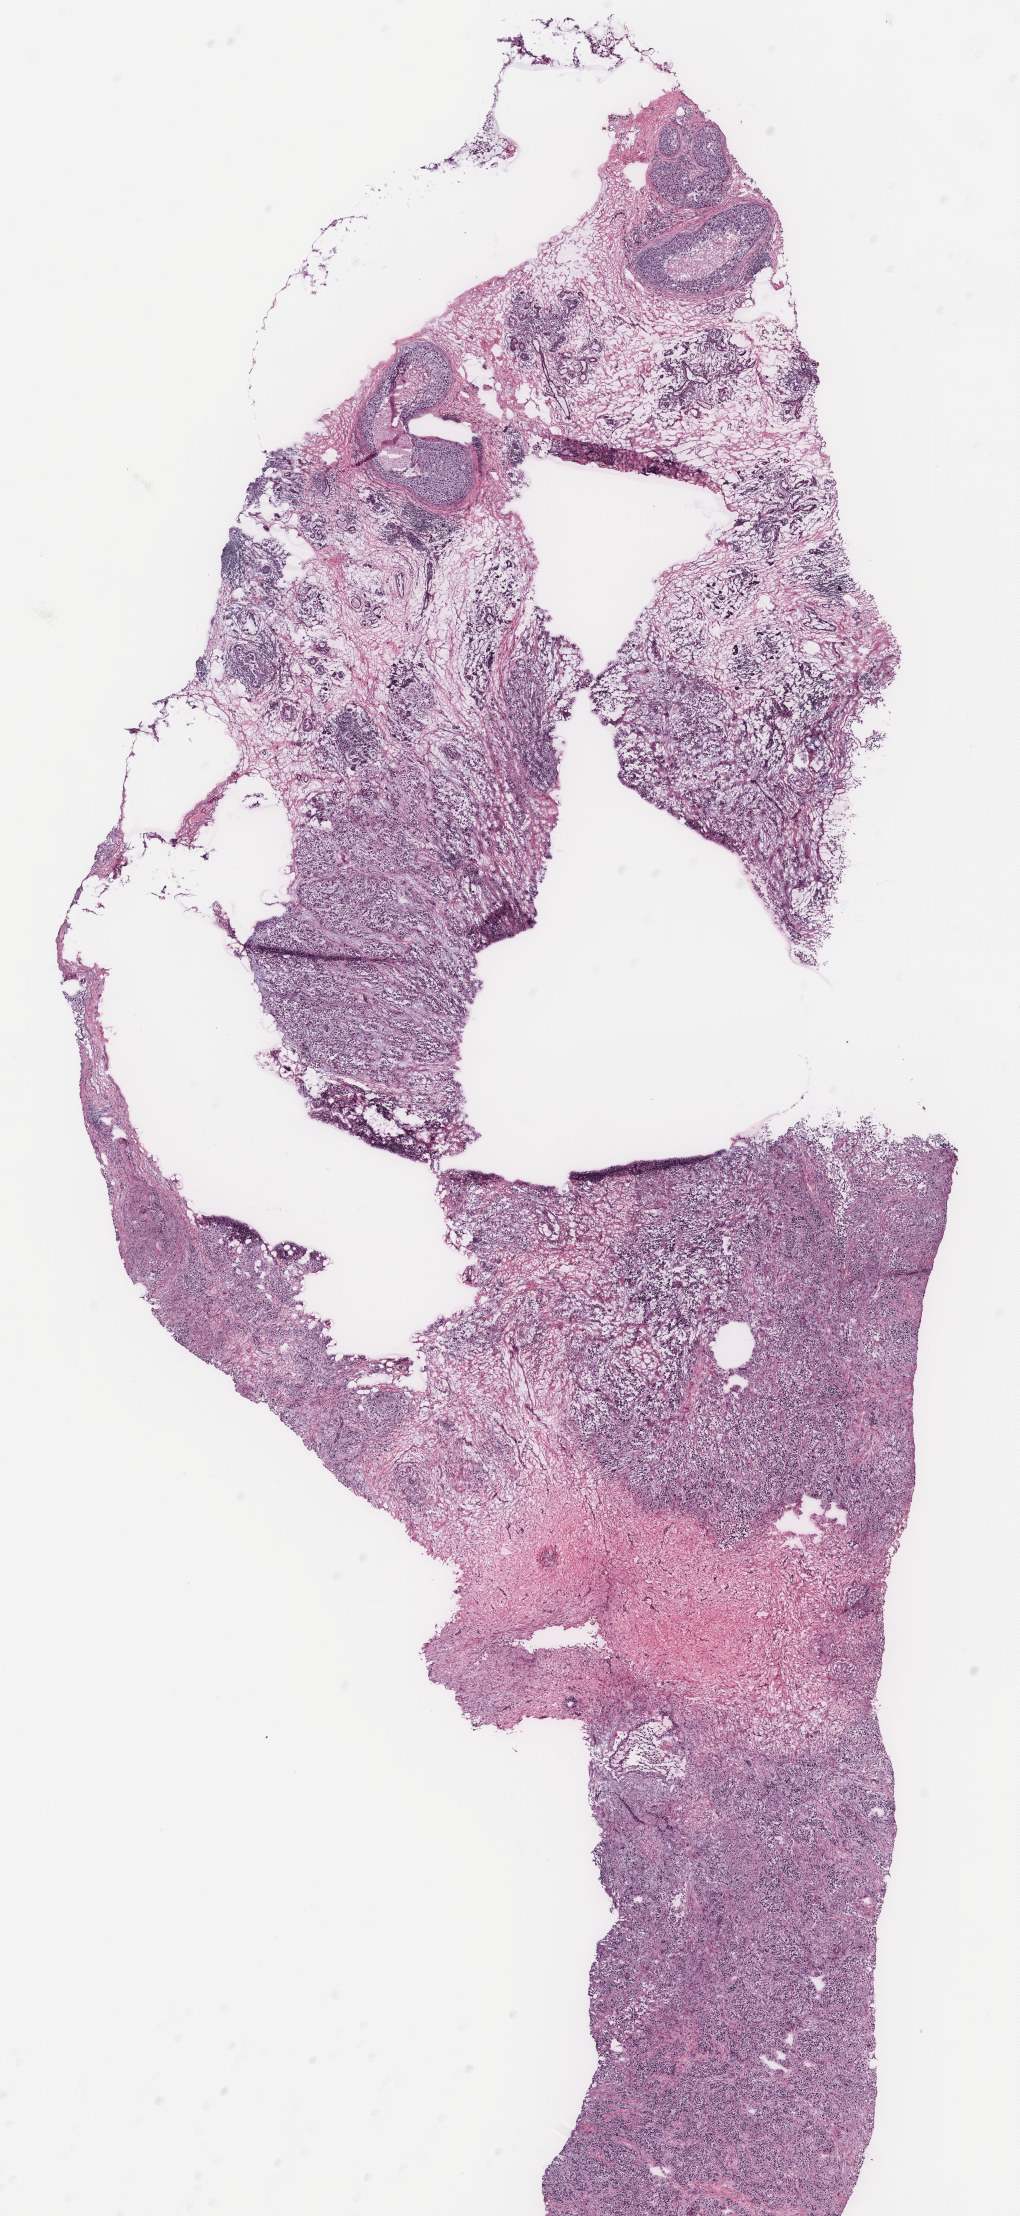
Digitized H&E tissue section (whole slide), low-resolution overview of the scanned area, about 8.2 x 17.7 mm (slide scanned at 40x); breast, tissue type not recorded. Female, 74 y/o.
• patient diagnosis: Infiltrating duct carcinoma, NOS